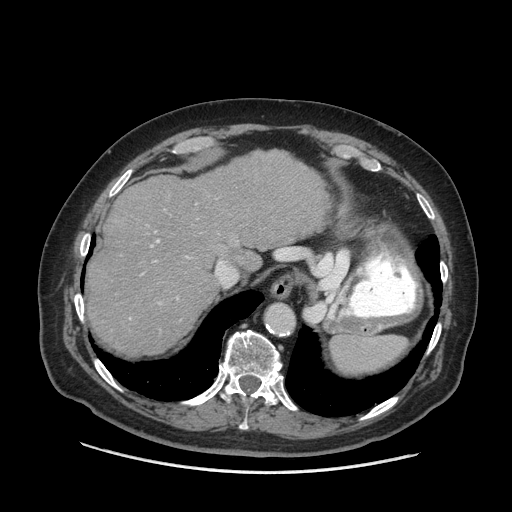
Contrast-enhanced abdominal CT (liver protocol), one axial slice. Slice 55 of 77 in the series (ordered by position). Reconstruction kernel STANDARD. Soft-tissue window (W 400 / L 40 HU). 512 × 512 image matrix, field of view 420 × 420 mm. Case-level facts recorded for this patient, not image findings: diagnosis: hepatocellular carcinoma (patient treated with transarterial chemoembolisation; whether this scan precedes or follows treatment is not stated here); TNM stage (as recorded): Stage-I; Child-Pugh class: A.
Annotated regions visible in this slice (semi-automatic segmentation, software-assisted and operator-edited):
- abdominal aorta: bounding box [x1, y1, x2, y2] px = [266, 304, 294, 333]
- liver parenchyma outside the tumour (the mass and vessels are separate outlines, so this box may not span the whole liver): [86, 150, 330, 354]
- mass: [104, 220, 119, 234]
- liver vessels: [151, 240, 160, 248]